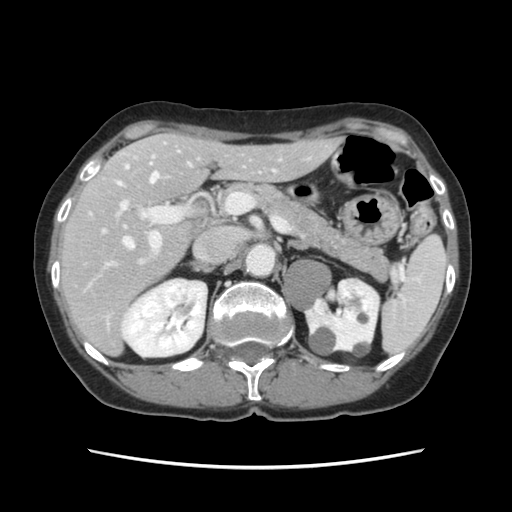
Contrast-enhanced abdominal CT, one axial slice. Position 73 of 120 along the scan axis. 120 kVp. Intravenous contrast given. Soft-tissue window (W 400 / L 40 HU). 2.5 mm slice thickness. 512 × 512 image matrix. Female patient, age 70 years. From the clinical record (not read from this slice): diagnosis: colorectal cancer liver metastases, imaged before liver resection; multiple liver metastases: no; largest metastasis: 2.5 cm.
Annotated regions visible in this slice (expert manual segmentation):
- hepatic veins: bounding box (x1, y1, x2, y2) in pixels: (103, 151, 179, 249)
- liver: (61, 134, 337, 353)
- planned liver remnant (the part of the liver to remain after resection): (90, 134, 338, 281)
- portal vein (with intrahepatic branches): (117, 143, 232, 264)